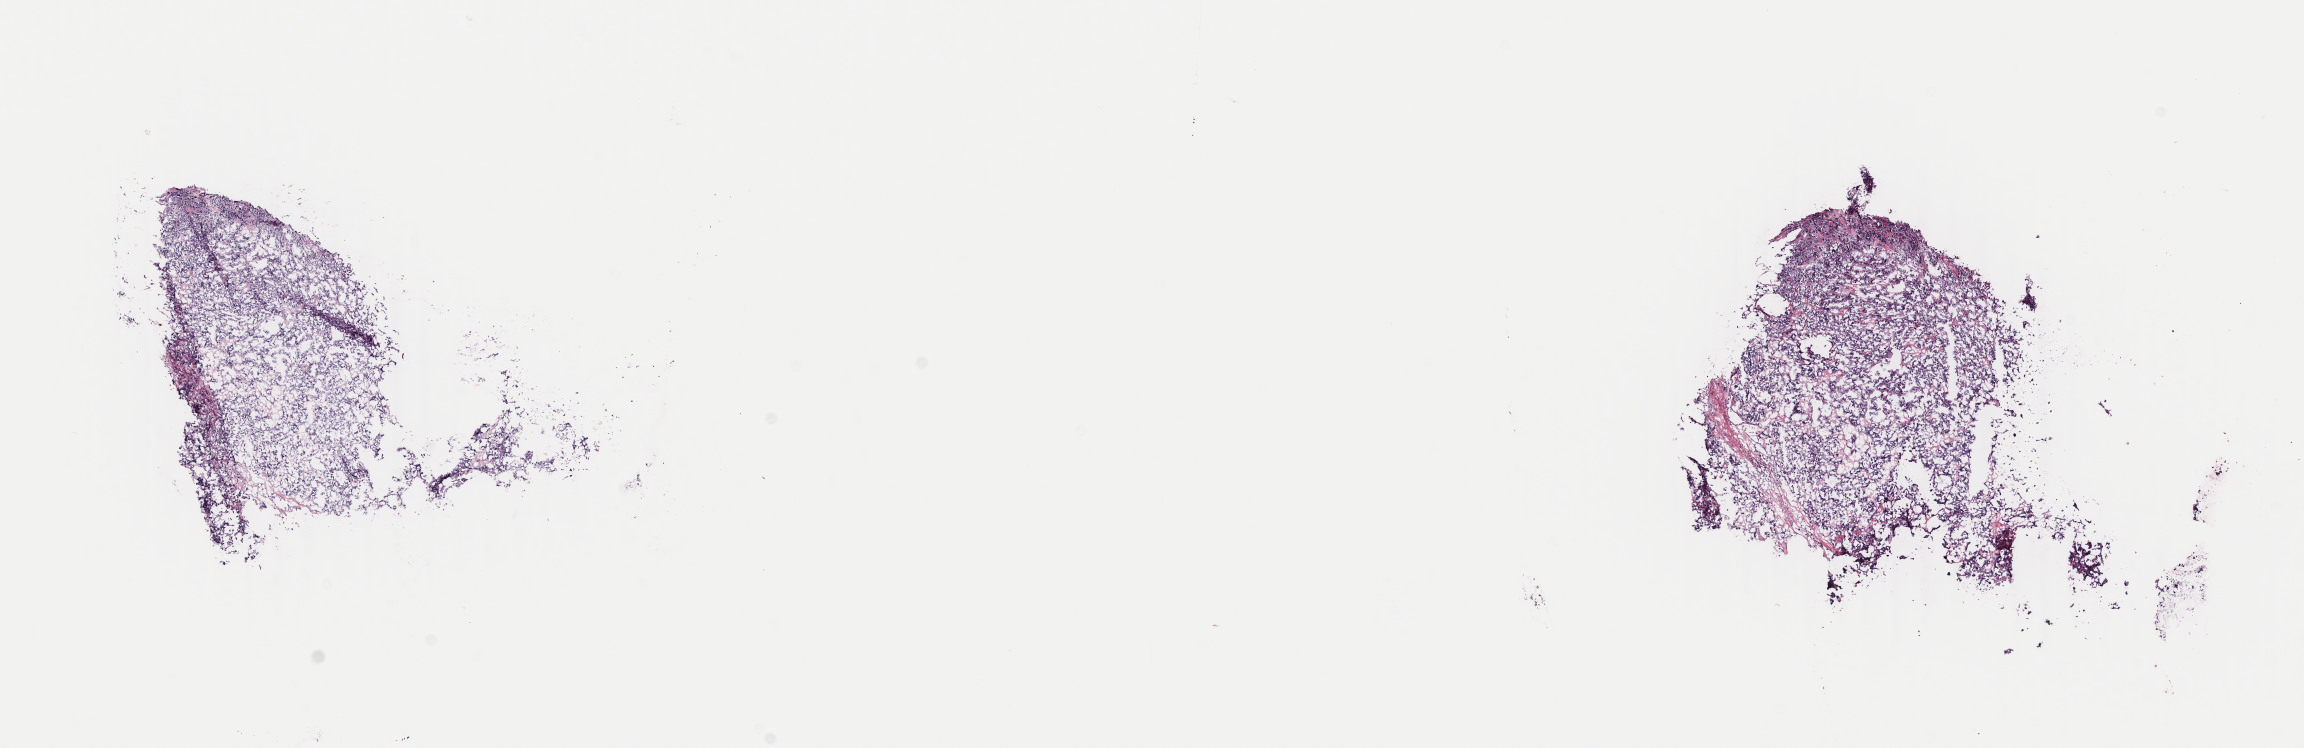
Hematoxylin and eosin (H&E) stained whole-slide image, whole scanned area (about 18.3 x 5.9 mm) shown as a low-resolution overview, frozen section from the top of the tissue portion, adrenal gland, primary tumour sample. Female, age 56 years at initial diagnosis. Pathologist review of this section (percent, as recorded): tumour cells 100%, tumour nuclei 95%, normal cells 0%, stromal cells 0%, necrosis 0%. Inflammatory infiltration, as recorded: lymphocyte infiltration 0%, monocyte infiltration 0%, neutrophil infiltration 0%.
- diagnosis: Pheochromocytoma, NOS
- laterality: right